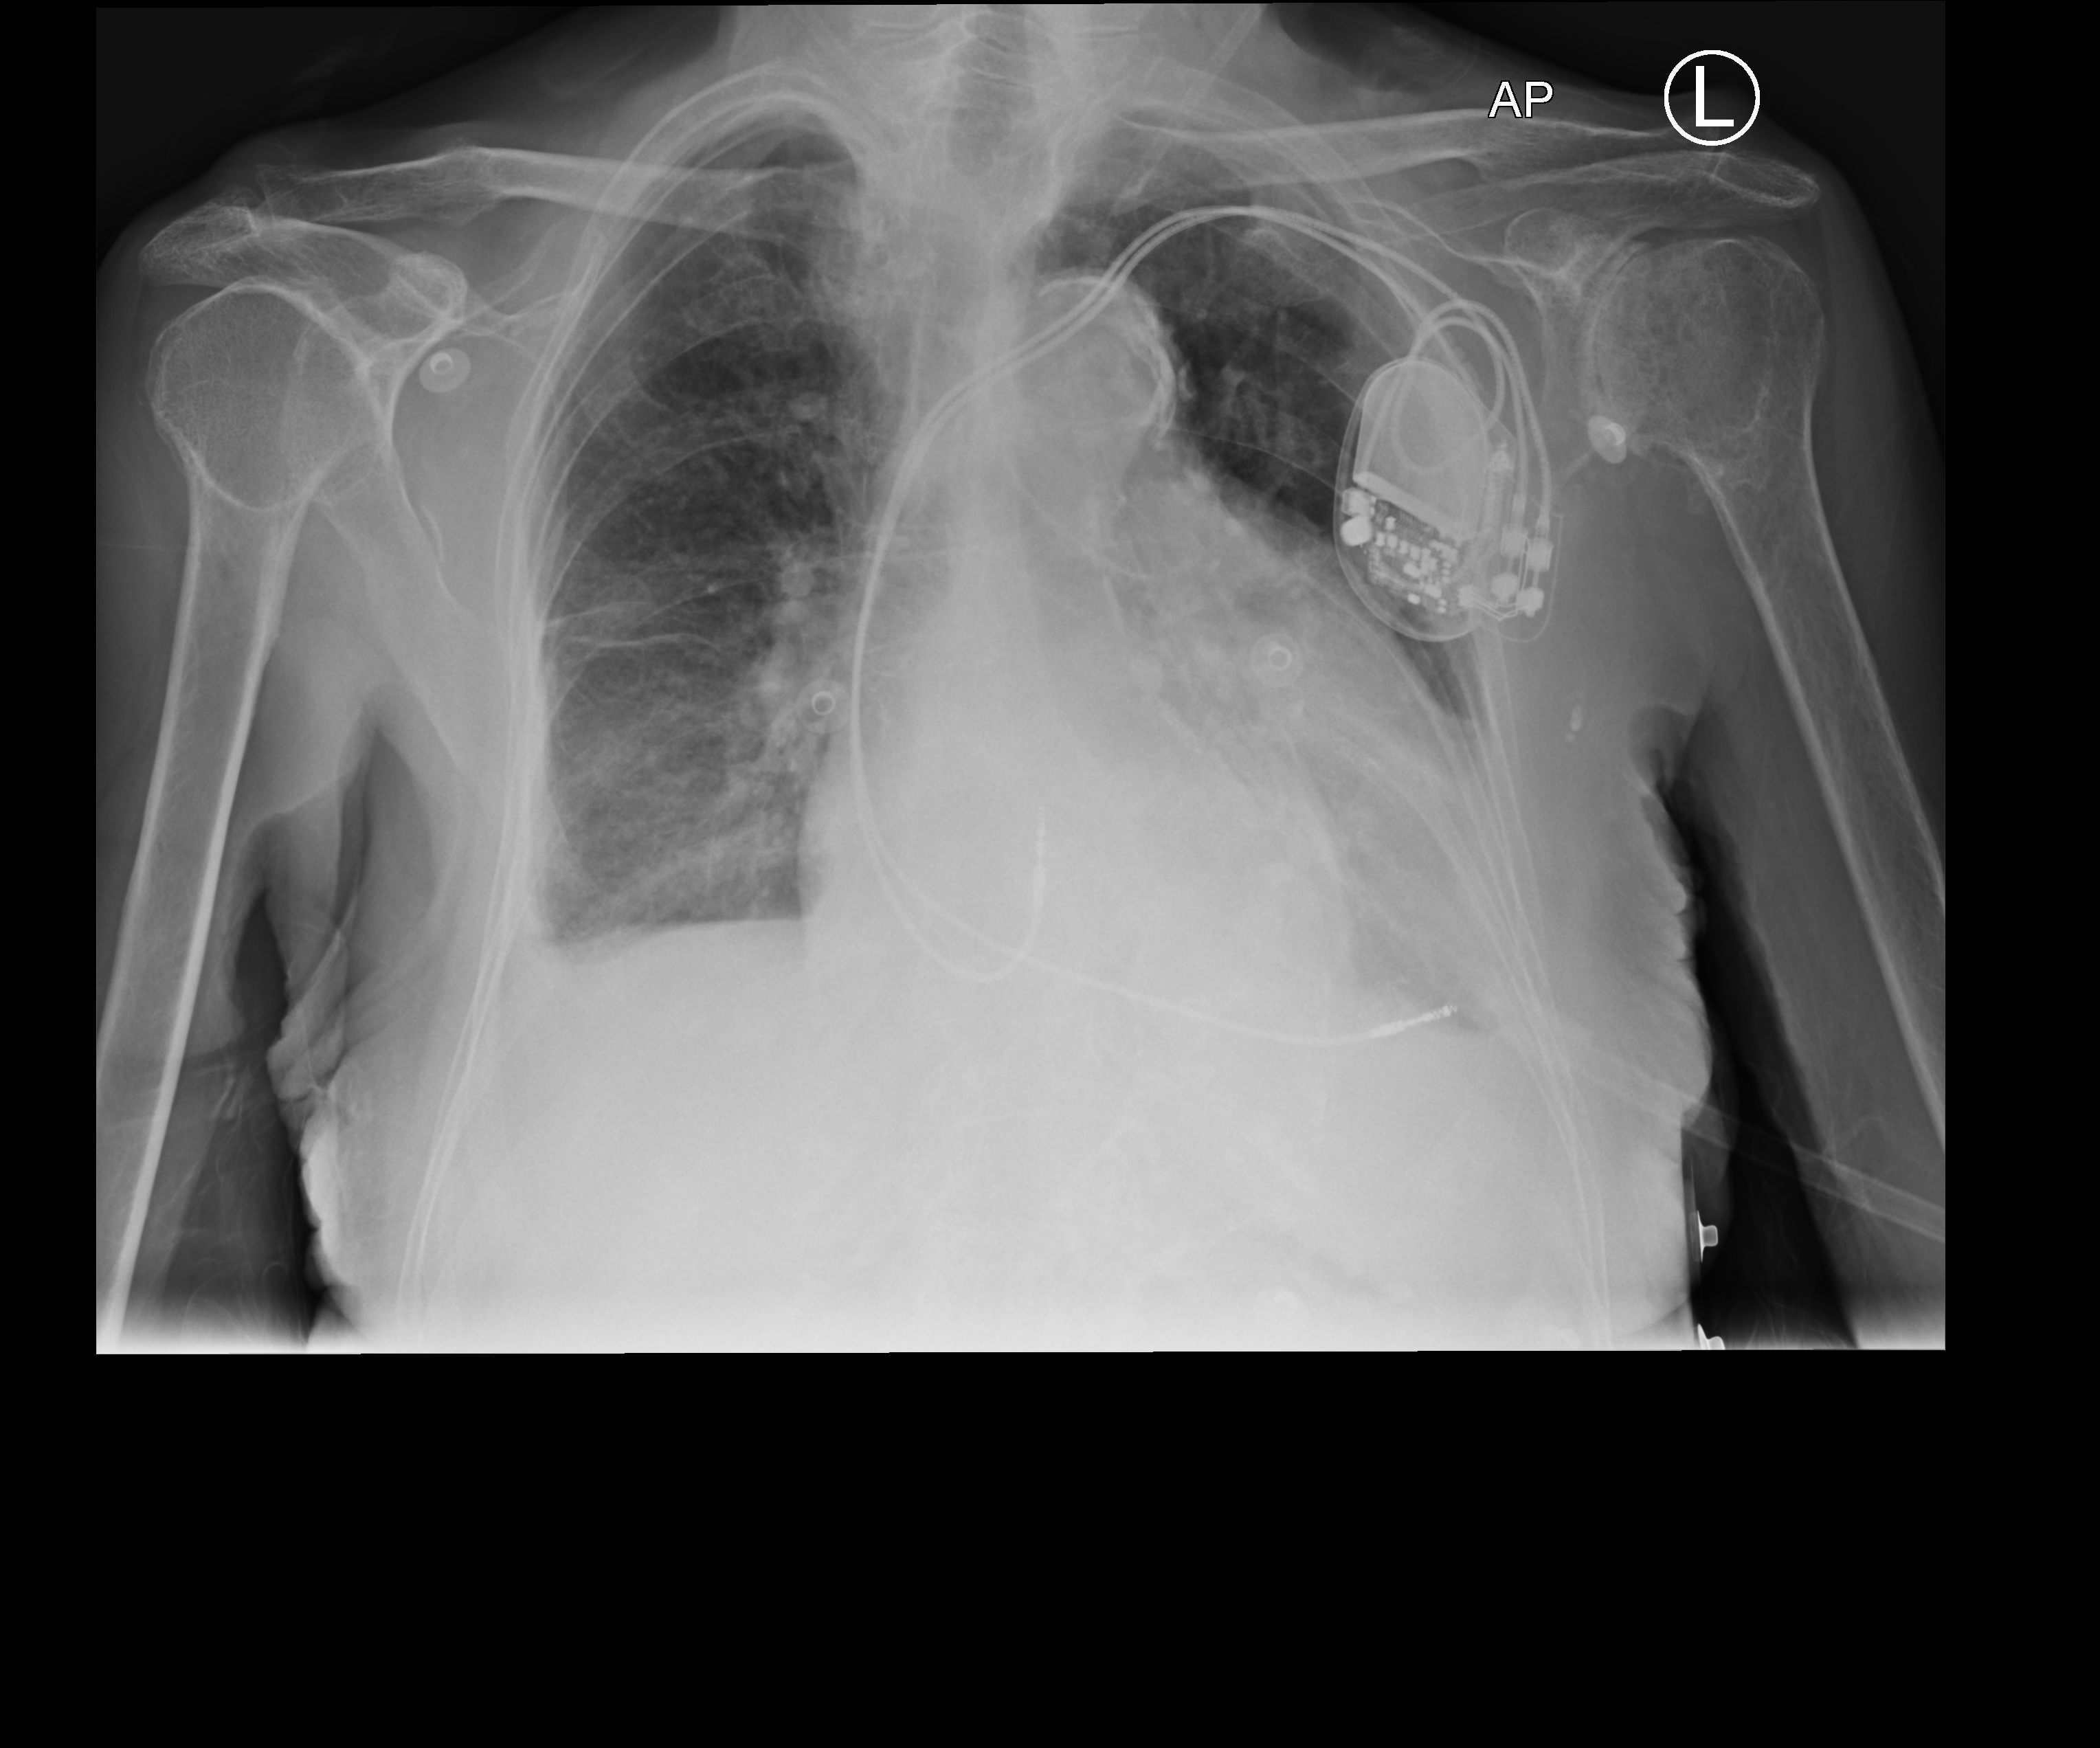
Chest radiograph; anteroposterior (AP) projection. Female patient hospitalised with COVID-19, age 75–90 years.
Admission-level facts for this patient (not findings on this image; timing relative to this image not recorded): admitted to intensive care during this hospital stay: no; COPD (admission record): no.